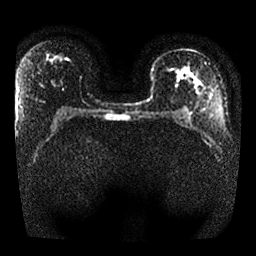
Breast MRI, one axial slice; position 14 of 25 along the scan axis; diffusion-weighted series; image 2 of 4 stored at this slice position (different b-values; order by instance number); 1.5 T; 256 × 256 image matrix. Female patient.
Structures marked on this image (expert manual segmentation):
- tumour on diffusion-weighted imaging: bounding box (x1, y1, x2, y2) in pixels: (175, 68, 186, 80)